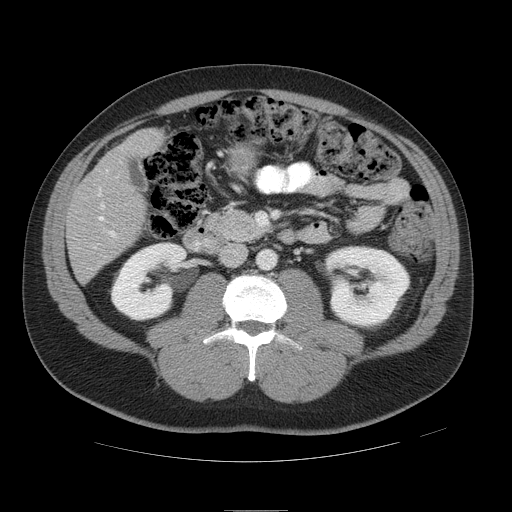
Contrast-enhanced abdominal CT, one axial slice; position 18 of 49 along the scan axis; reconstruction kernel STANDARD; 120 kVp; intravenous contrast given; soft-tissue window (W 400 / L 40 HU); 512 × 512 image matrix, field of view 425 × 425 mm. Male patient, age 52 years. From the clinical record (not read from this slice): diagnosis: colorectal cancer liver metastases, imaged before liver resection; multiple liver metastases: yes; largest metastasis: 5.1 cm; disease in both lobes: yes.
Annotated regions visible in this slice (outlined manually by an expert reader):
- hepatic veins: bounding box <98,203,105,221> (left, top, right, bottom; pixels)
- liver: <68,132,159,280>
- planned liver remnant (the part of the liver to remain after resection): <142,133,160,144>
- portal vein (with intrahepatic branches): <94,169,118,248>